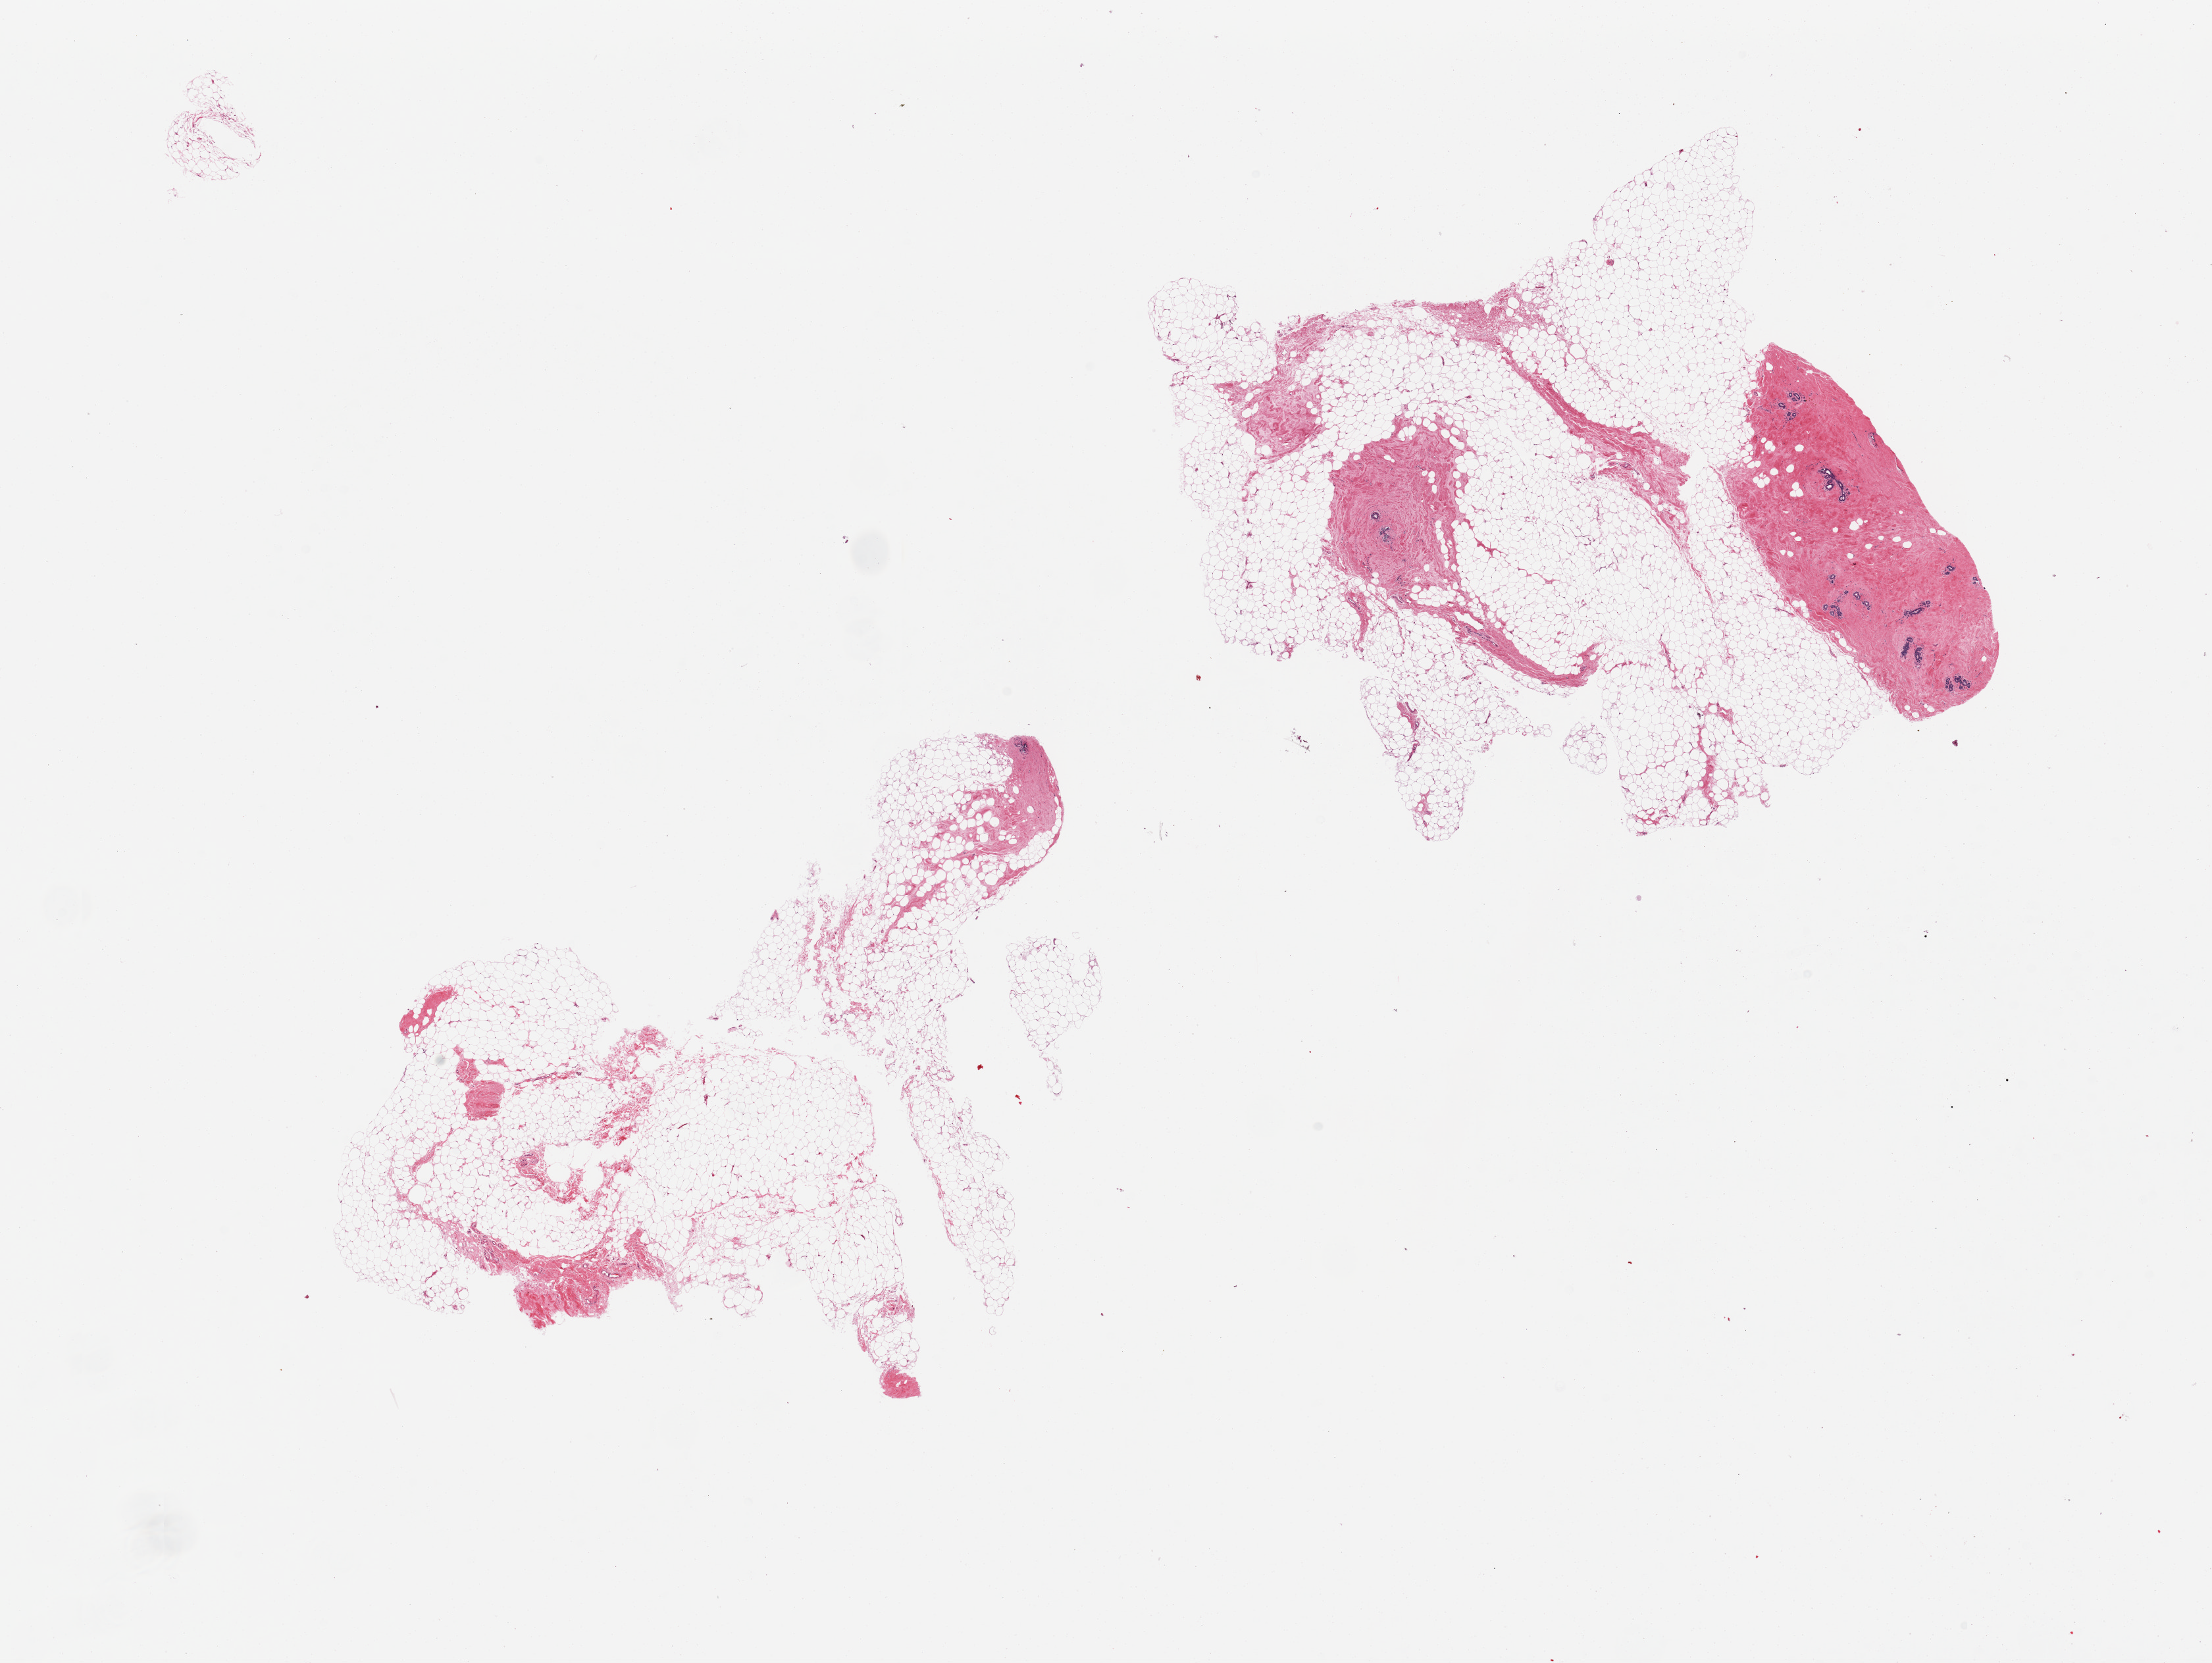
Haematoxylin and eosin whole-slide image, brightfield — shown as a low-resolution overview of the whole scanned area (about 26.6 x 20.0 mm); PAXgene-fixed, paraffin-embedded tissue; sampled site (target tissue): breast; tissue donor sample.
- reviewer comment on this tissue sample: 2 pieces, mainly fibroadipose; a few atrophic ductal elements noted